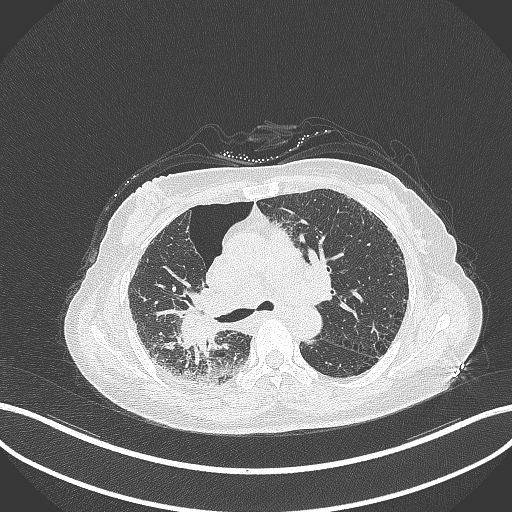
Chest CT, one axial slice; slice 216 of 408 in the series (ordered by position); 120 kVp; lung window (W 1500 / L -600 HU); 1 mm slice thickness; 512 × 512 image matrix, field of view 400 × 400 mm. Patient: female, 64 years. Case-level facts recorded for this patient, not image findings: clinical TNM (as recorded): T3 N3 M0.
Structures marked on this image (bounding box drawn by a radiologist):
- lung tumour (recorded histology: squamous cell carcinoma): bounding box [x1, y1, x2, y2] px = [171, 290, 230, 357]